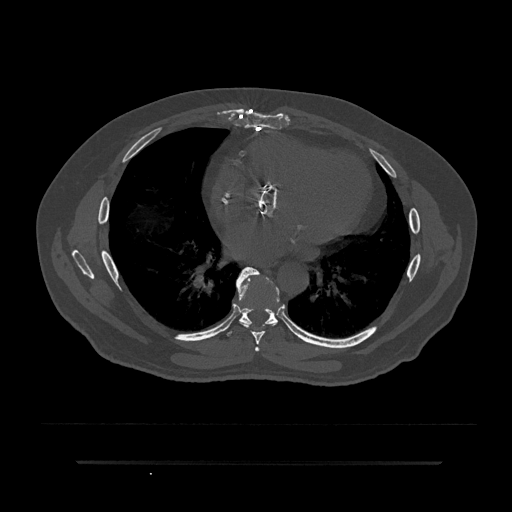
CT including the spine, one axial slice. Slice 456 of 797 in the series (ordered by position). Reconstruction kernel Br40s/3. 120 kVp. Bone window (W 1800 / L 400 HU). 0.5 mm slice thickness. 512 × 512 image matrix, field of view 464 × 464 mm. Male patient, age 59 years. Case-level facts recorded for this patient, not image findings: primary cancer: bile ducts; vertebrae with lytic lesions (as recorded): T10.
Outlined on this slice (semi-automatically segmented with operator editing):
- T6 vertebra: bounding box <255,347,260,352> (left, top, right, bottom; pixels)
- T7 vertebra: <236,267,279,345>
- T8 vertebra: <224,283,296,336>